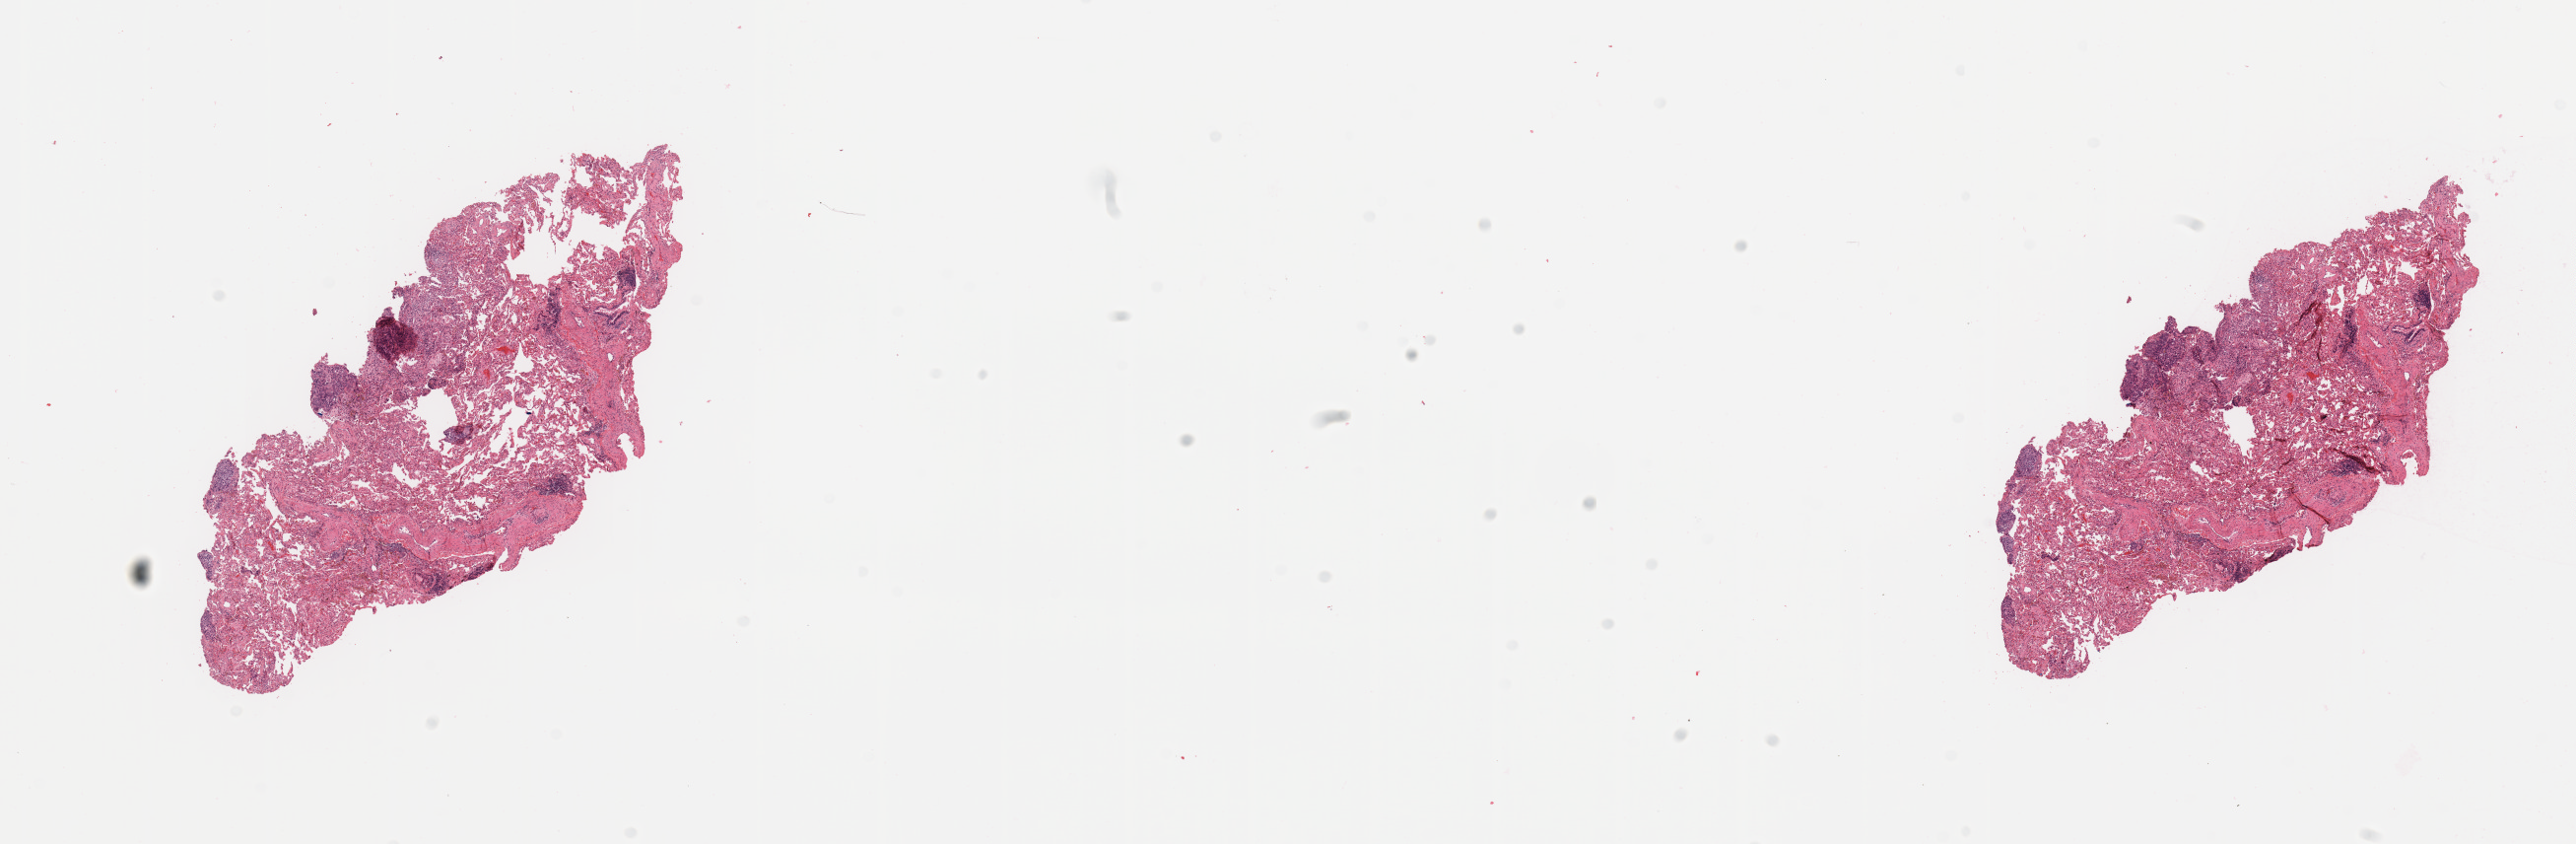
Whole-slide histology image, H&E-stained, a low-resolution overview of the entire scanned area, about 20.7 x 6.8 mm (acquisition: 20x scan); tumour tissue sample, lung. Female, 64 y/o.
Diagnosis: Squamous cell carcinoma, NOS.